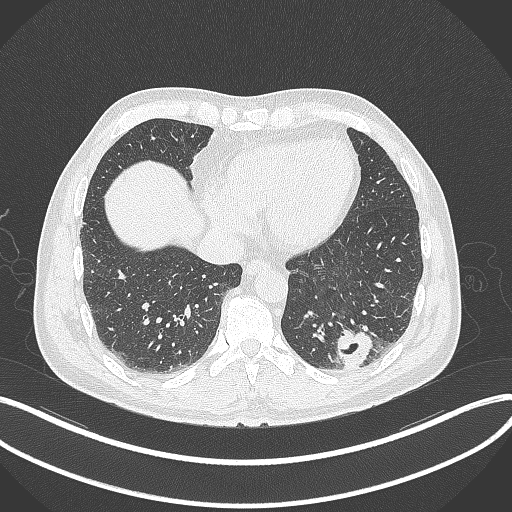
Chest CT, one axial slice. Position 79 of 300 along the scan axis. Reconstruction kernel B70f. Lung window (W 1500 / L -600 HU). 512 × 512 image matrix, field of view 400 × 400 mm. Patient: male, 54 years. Case-level facts recorded for this patient, not image findings: clinical TNM (as recorded): T1c N0 M1.
Outlined on this slice (rectangle marked by the reading radiologist):
- lung tumour (recorded histology: adenocarcinoma): box from (x=335, y=328) to (x=373, y=369) px